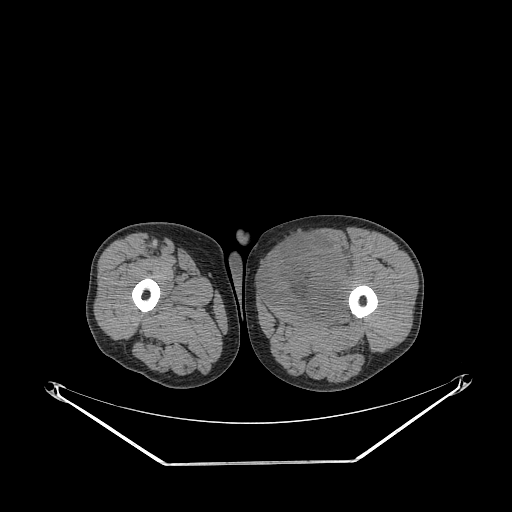
CT of an extremity soft-tissue mass (from a PET/CT study), one axial slice; slice 248 of 267 in the series (ordered by position); 140 kVp; soft-tissue window (W 400 / L 40 HU); 3.75 mm slice thickness; 512 × 512 image matrix, field of view 500 × 500 mm. Male patient. Case-level facts recorded for this patient, not image findings: histological type: pleiomorphic liposarcoma; grade: high; site of the primary tumour: left thigh.
Outlined on this slice (expert contour drawn on MRI and transferred to this co-registered scan by the dataset authors):
- gross tumour volume including surrounding oedema: bounding box (x1, y1, x2, y2) in pixels: (263, 235, 355, 318)
- gross tumour volume (mass): (263, 235, 352, 318)